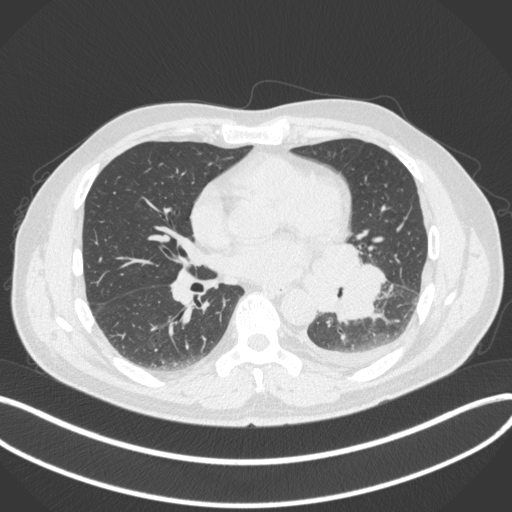
Chest CT, one axial slice; position 170 of 350 along the scan axis; reconstruction kernel B31f; 120 kVp; lung window (W 1500 / L -600 HU); 1 mm slice thickness; 512 × 512 image matrix, field of view 400 × 400 mm. Male patient, age 58 years. Case-level facts recorded for this patient, not image findings: clinical TNM (as recorded): T3 N1 M1b; histopathological grade: G3.
Annotated regions visible in this slice (rectangle marked by the reading radiologist):
- lung tumour (recorded histology: small cell carcinoma): bounding box [x1, y1, x2, y2] px = [312, 243, 390, 328]